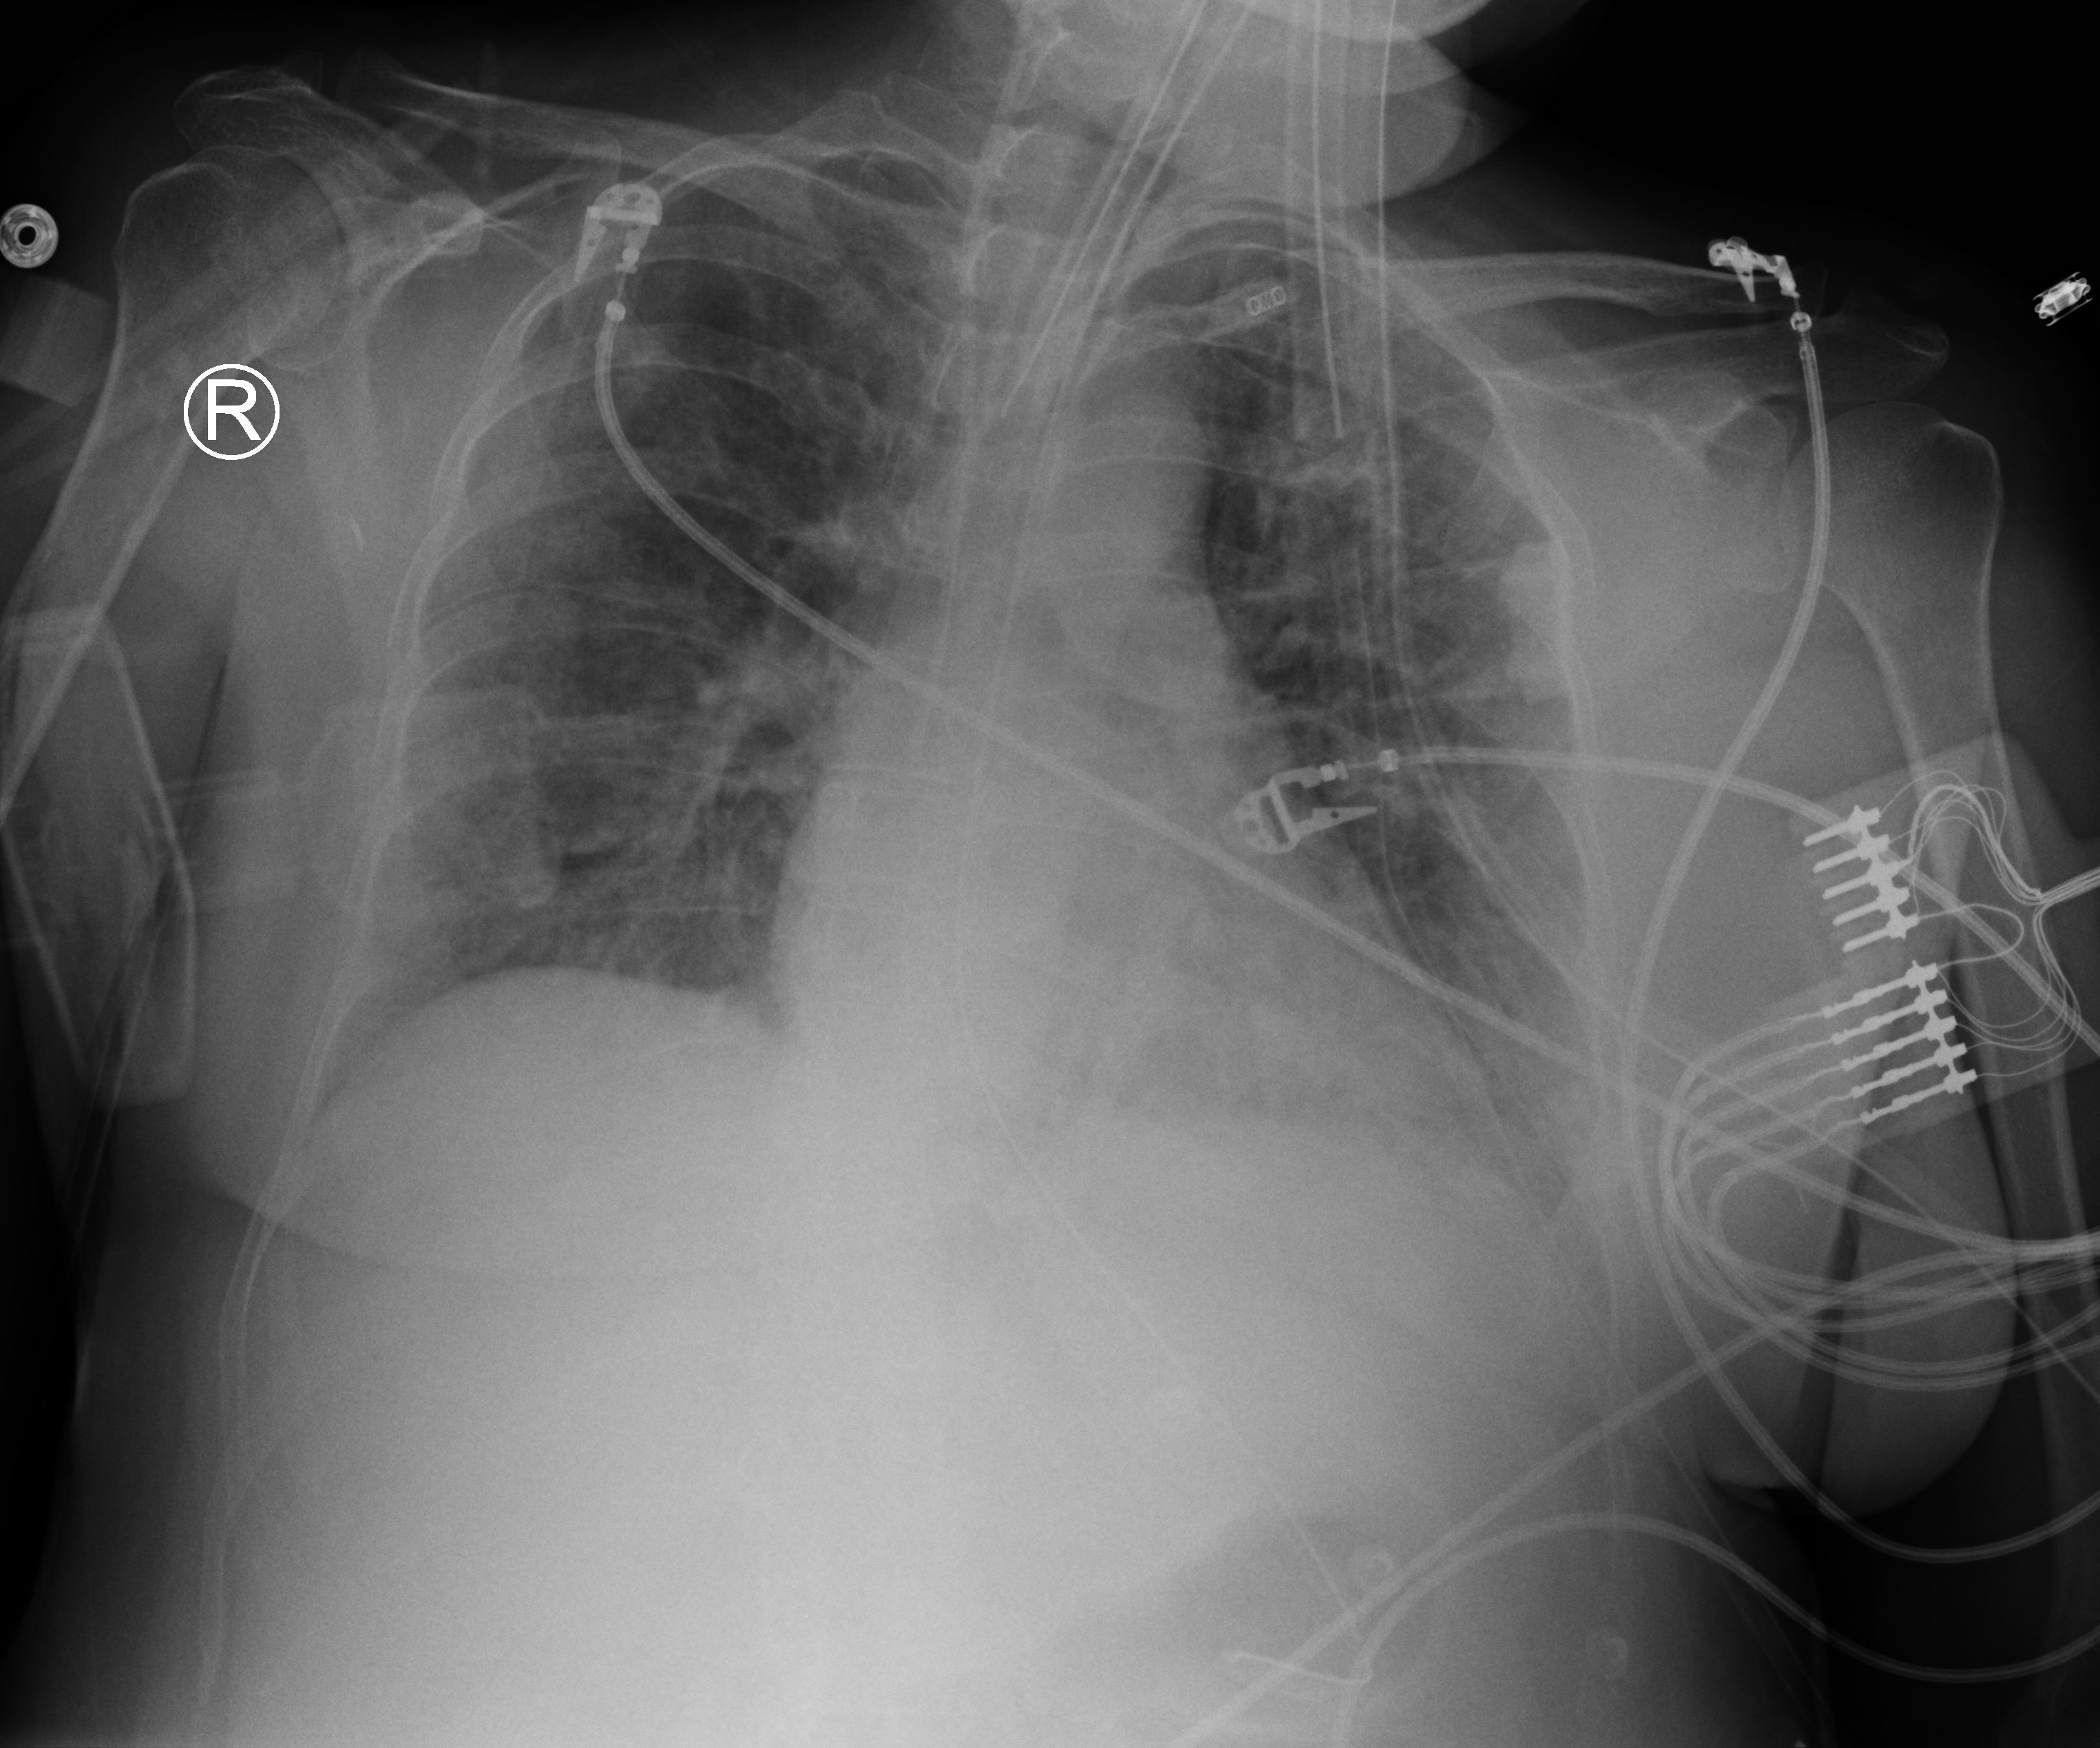
Portable chest radiograph; anteroposterior (AP) projection. Patient hospitalised with COVID-19; female, aged 18–59 years.
Admission-level facts for this patient (not findings on this image; timing relative to this image not recorded): mechanically ventilated during this hospital stay: yes; chronic kidney disease (admission record): no; diabetes (admission record): no.